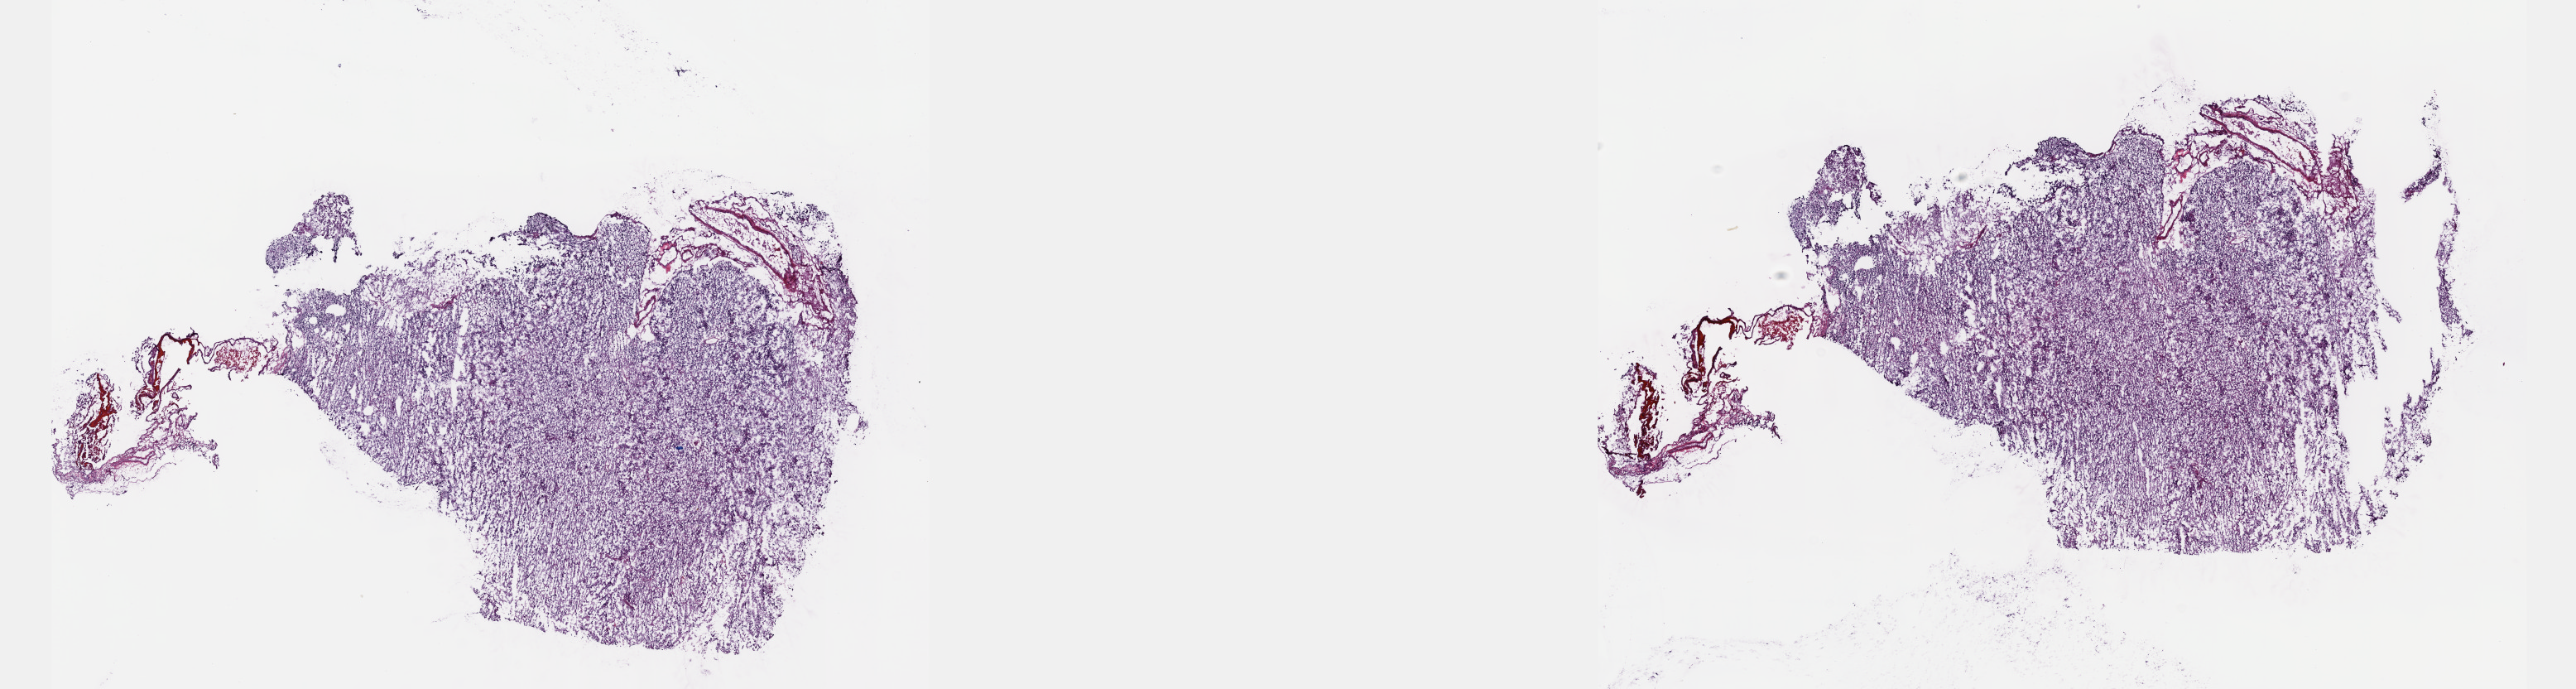
Whole-slide histology image, H&E, a low-resolution overview of the entire scanned area, about 25.1 x 6.7 mm, frozen section, brain, primary tumour sample. Patient: female, age at initial diagnosis 26 years. Histologic grade: G3 (poorly differentiated). Pathologist review of this section (percent, as recorded): tumour cells 70%, tumour nuclei 90%, normal cells 10%, stromal cells 20%, necrosis 0%. Inflammatory infiltration, as recorded: lymphocyte infiltration 0%, monocyte infiltration 0%, neutrophil infiltration 0%.
• laterality: left
• diagnosis: Mixed glioma